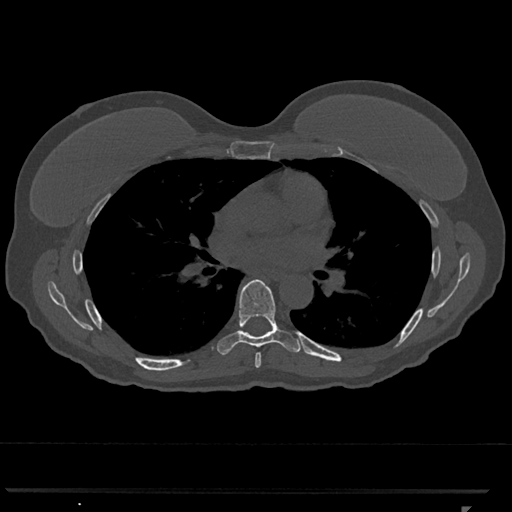
CT including the spine, one axial slice; reconstruction kernel Br40s/3; 120 kVp; bone window (W 1800 / L 400 HU); 0.5 mm slice thickness; 512 × 512 image matrix, field of view 380 × 380 mm. Patient: female, 62 years. Case-level facts recorded for this patient, not image findings: primary cancer: renal.
Structures marked on this image (semi-automatic segmentation, software-assisted and operator-edited):
- T6 vertebra: bounding box [x1, y1, x2, y2] px = [255, 353, 261, 368]
- T7 vertebra: [217, 279, 302, 355]